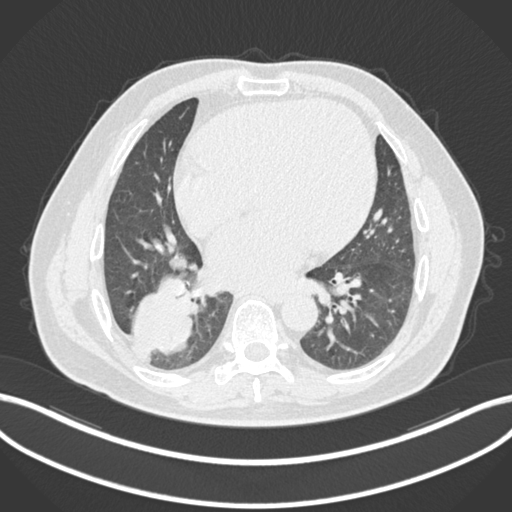
Chest CT, one axial slice; slice 68 of 200 in the series (ordered by position); 120 kVp; lung window (W 1500 / L -600 HU); 1 mm slice thickness; 512 × 512 image matrix, field of view 400 × 400 mm. Patient: male, 59 years.
Outlined on this slice (rectangle marked by the reading radiologist):
- lung tumour (recorded histology: adenocarcinoma): bounding box [x1, y1, x2, y2] px = [134, 269, 197, 356]